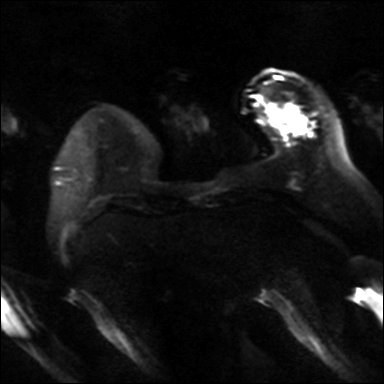
Breast MRI, one axial slice. Diffusion-weighted series; image 2 of 4 stored at this slice position (different b-values; order by instance number). 3 T. 4 mm slice thickness. 384 × 384 image matrix, field of view 320 × 320 mm. Female patient.
Structures marked on this image (outlined manually by an expert reader):
- tumour on diffusion-weighted imaging: box from (x=270, y=111) to (x=312, y=135) px